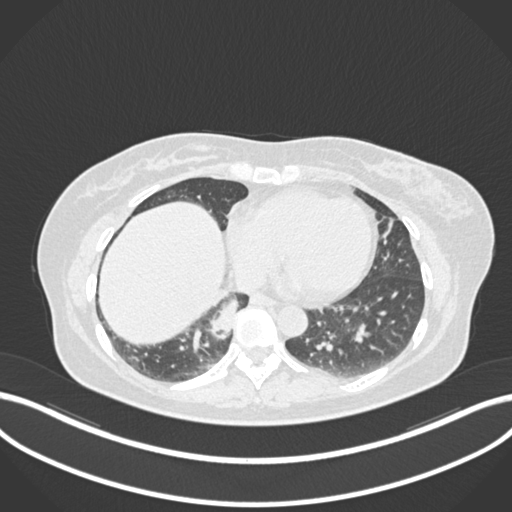
Chest CT, one axial slice; slice 546 of 677 in the series (ordered by position); reconstruction kernel B30f; 120 kVp; lung window (W 1500 / L -600 HU); 512 × 512 image matrix, field of view 400 × 400 mm. Patient: female, 54 years. Case-level facts recorded for this patient, not image findings: clinical TNM (as recorded): T4 N0 M0.
Annotated regions visible in this slice (rectangle marked by the reading radiologist):
- lung tumour (recorded histology: adenocarcinoma): box from (x=198, y=287) to (x=241, y=345) px